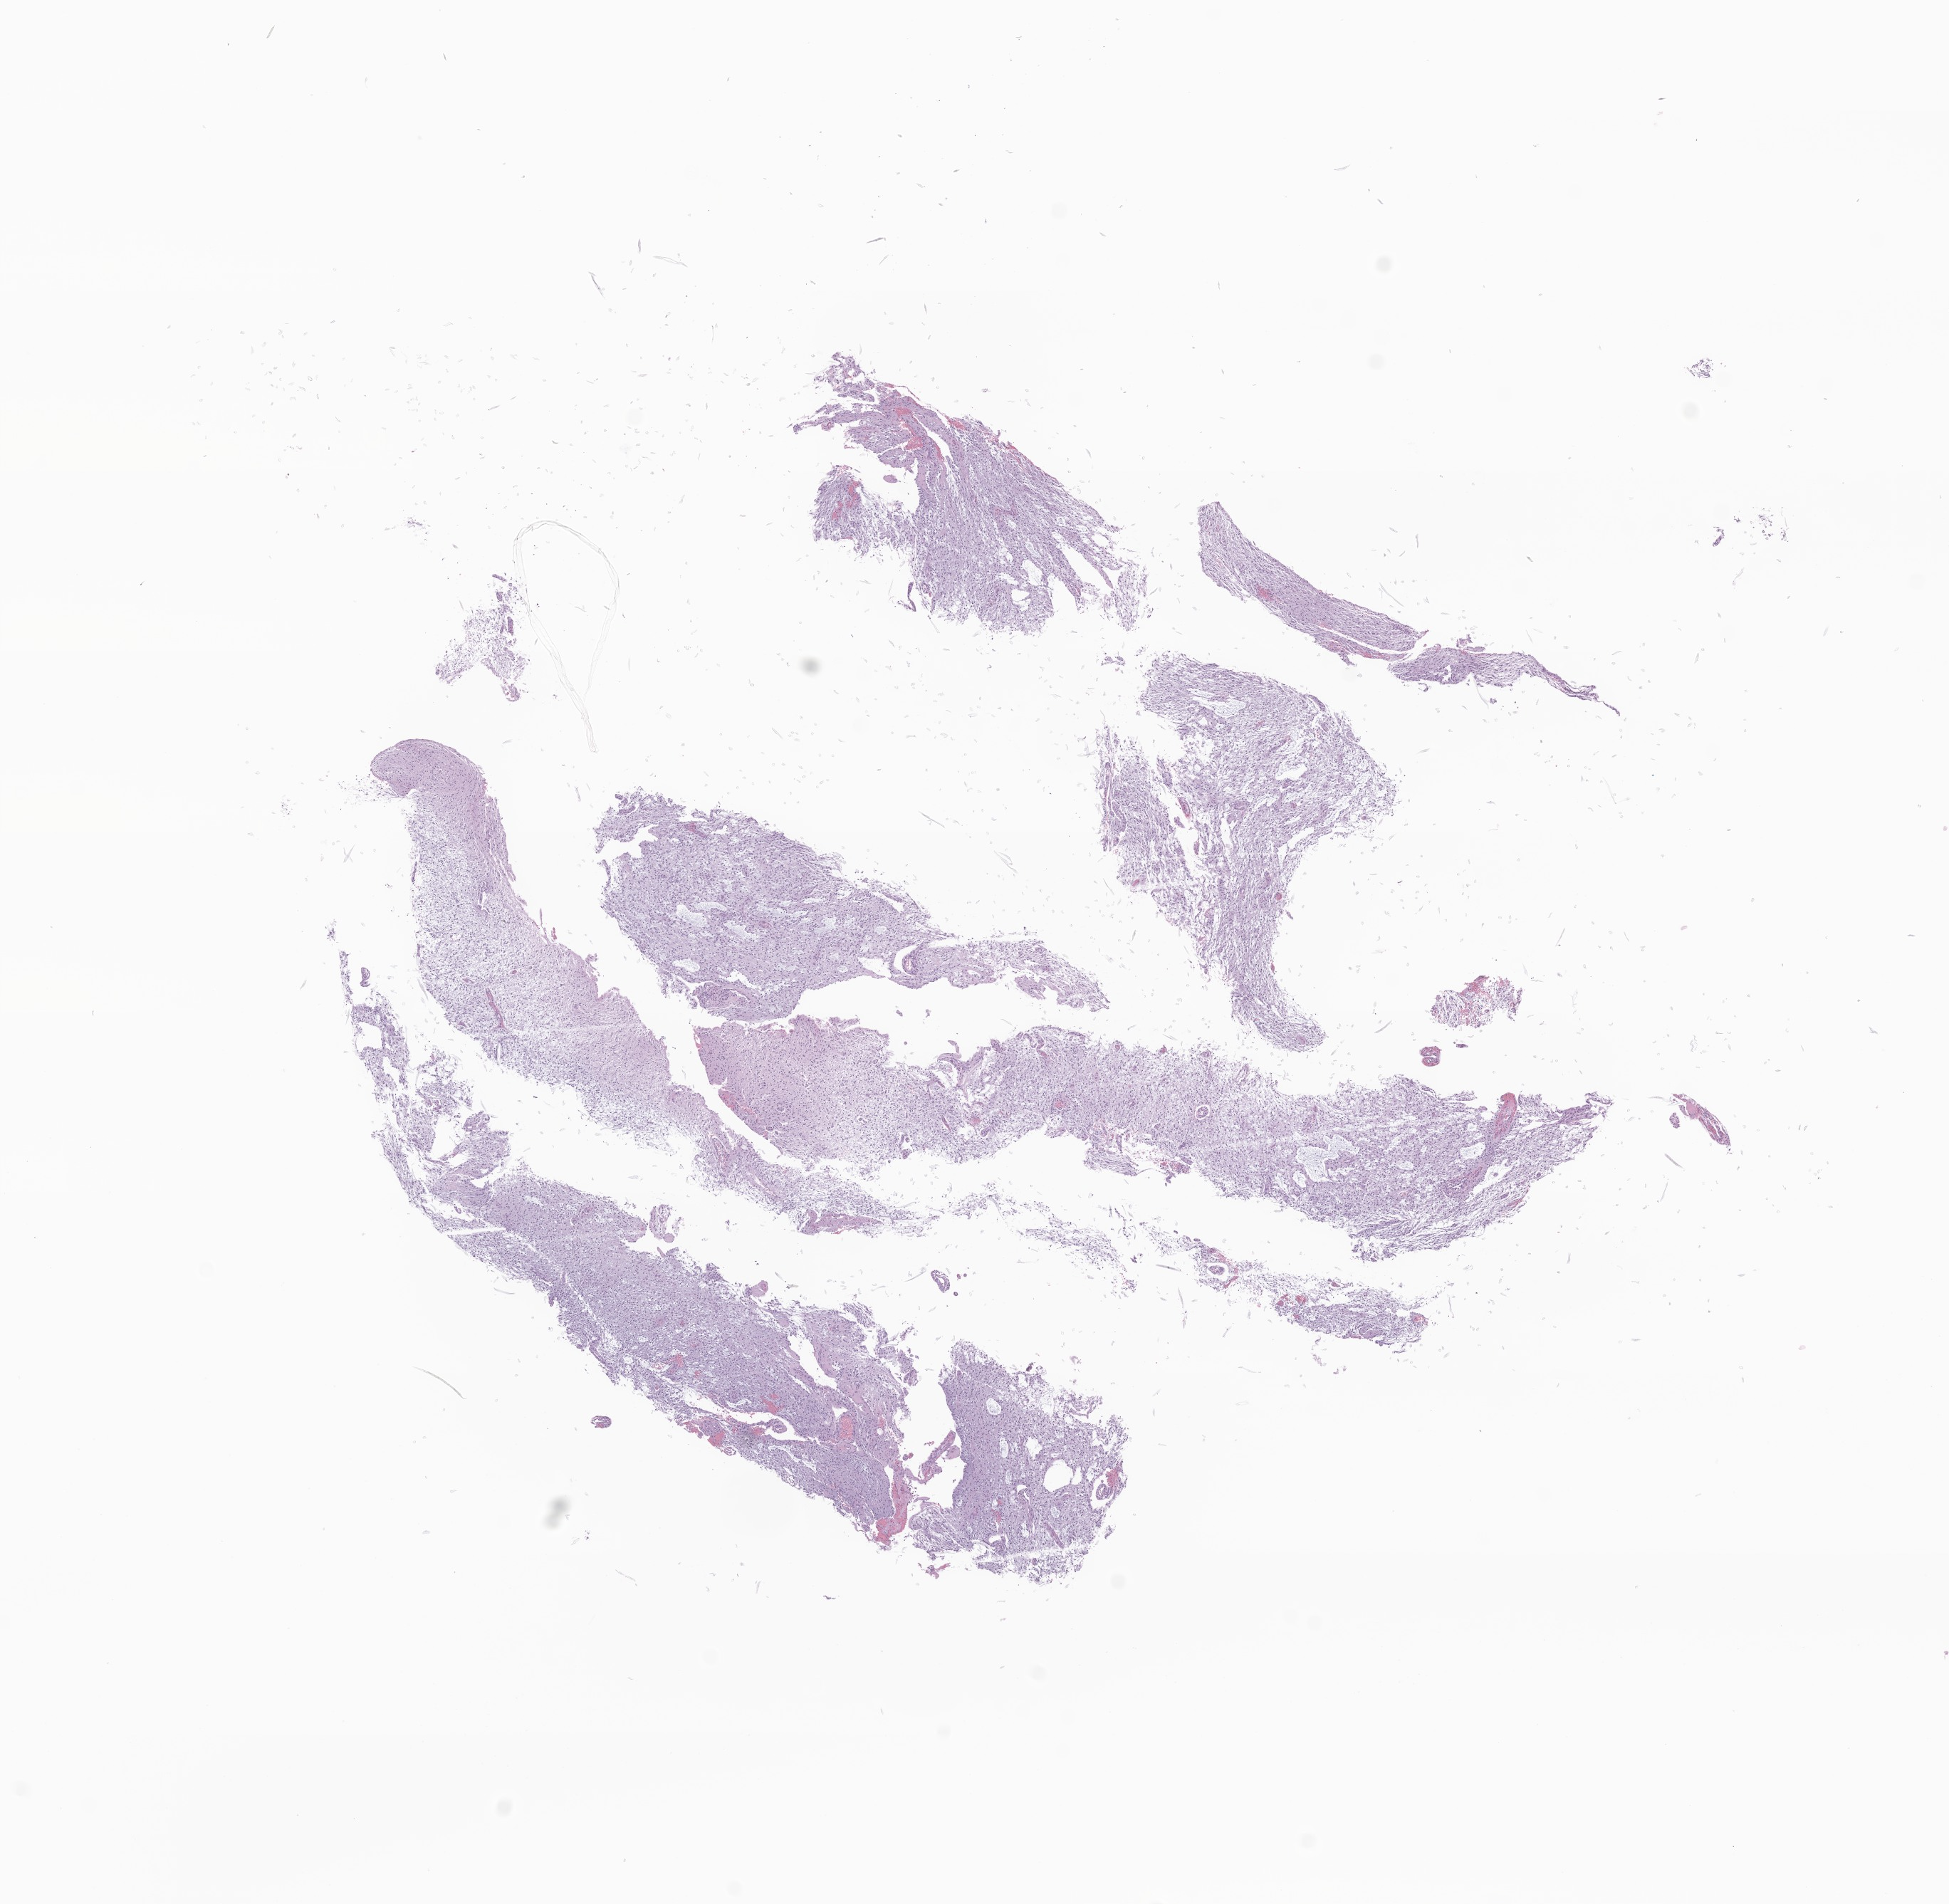
Whole-slide image, hematoxylin and eosin (H&E) stain of tumor tissue from the cerebellum — whole scanned area (about 11.5 x 11.3 mm) shown as a low-resolution overview; FFPE section. Male patient, age 59 months.
• diagnosis (ICD-O-3 morphology term): Ependymoma, NOS